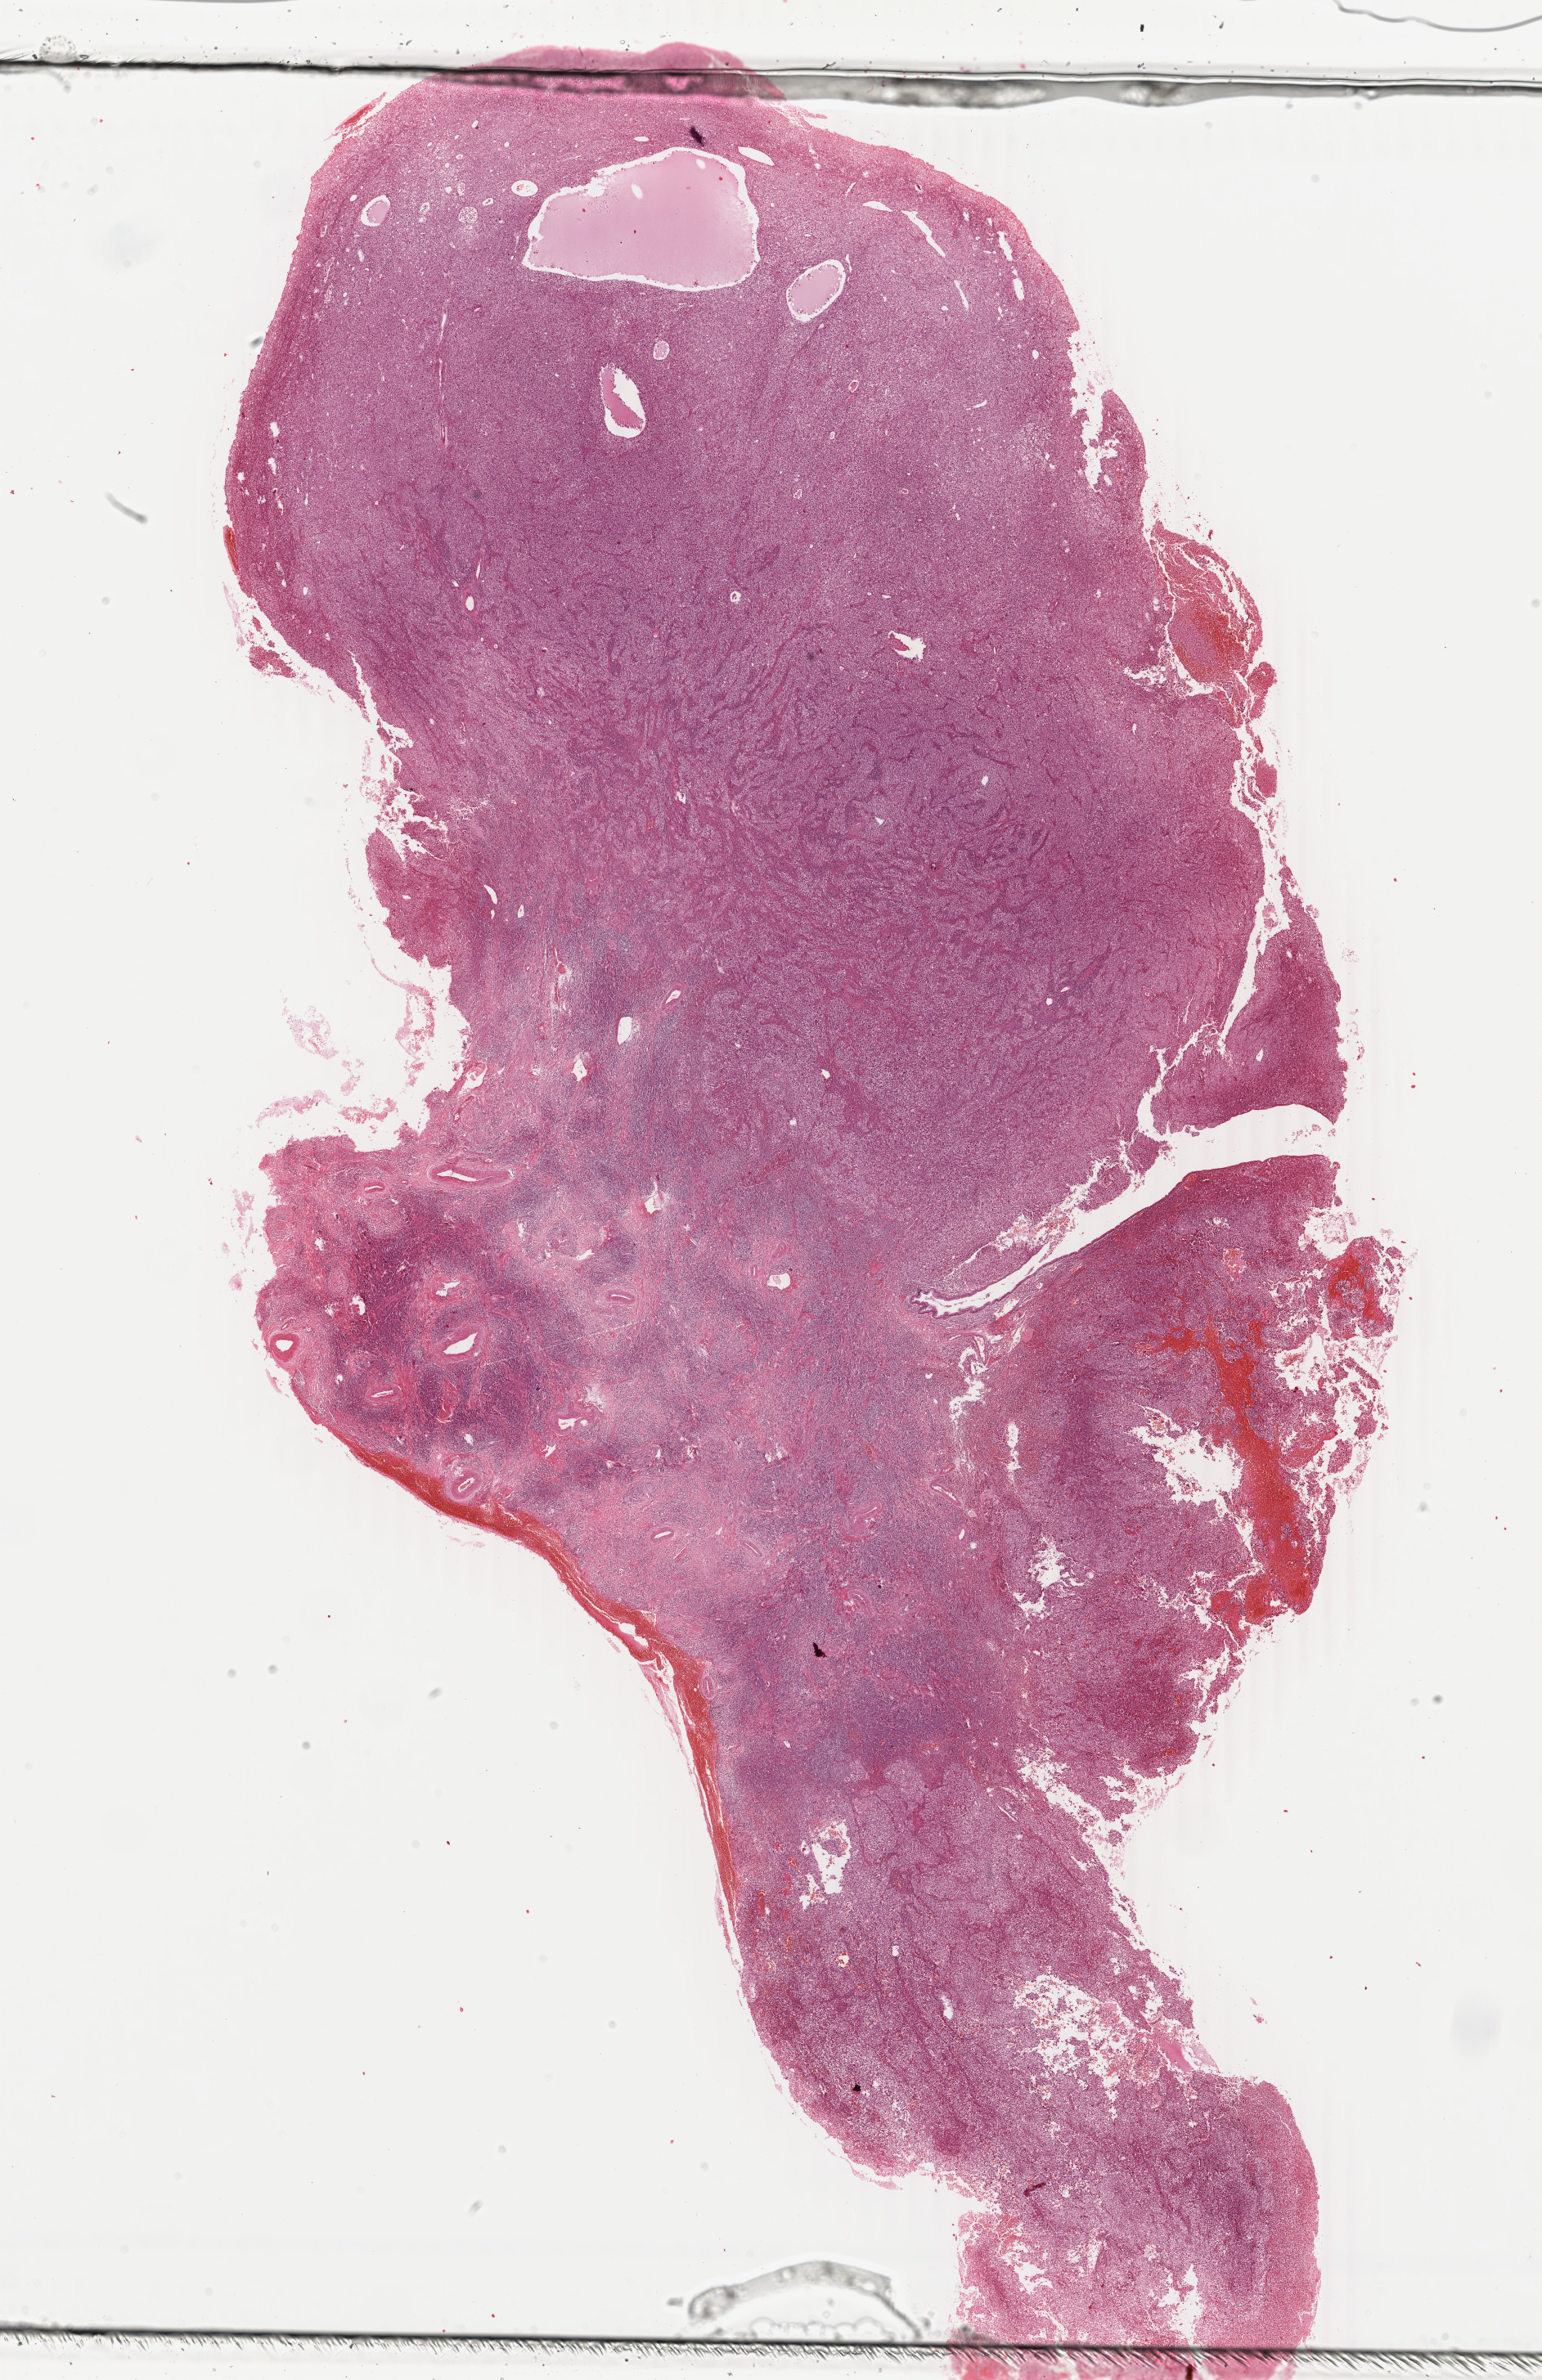
Digitized H&E tissue section (whole slide), whole scanned area (about 15.0 x 23.1 mm) shown as a low-resolution overview. Formalin-fixed paraffin-embedded (FFPE) diagnostic section. Sample: primary tumour, cervix. Female patient; age at initial diagnosis 45 years. Histologic grade: G3 (poorly differentiated).
FIGO stage: IB1. Pathologic diagnosis: Squamous cell carcinoma, NOS (cervix uteri).